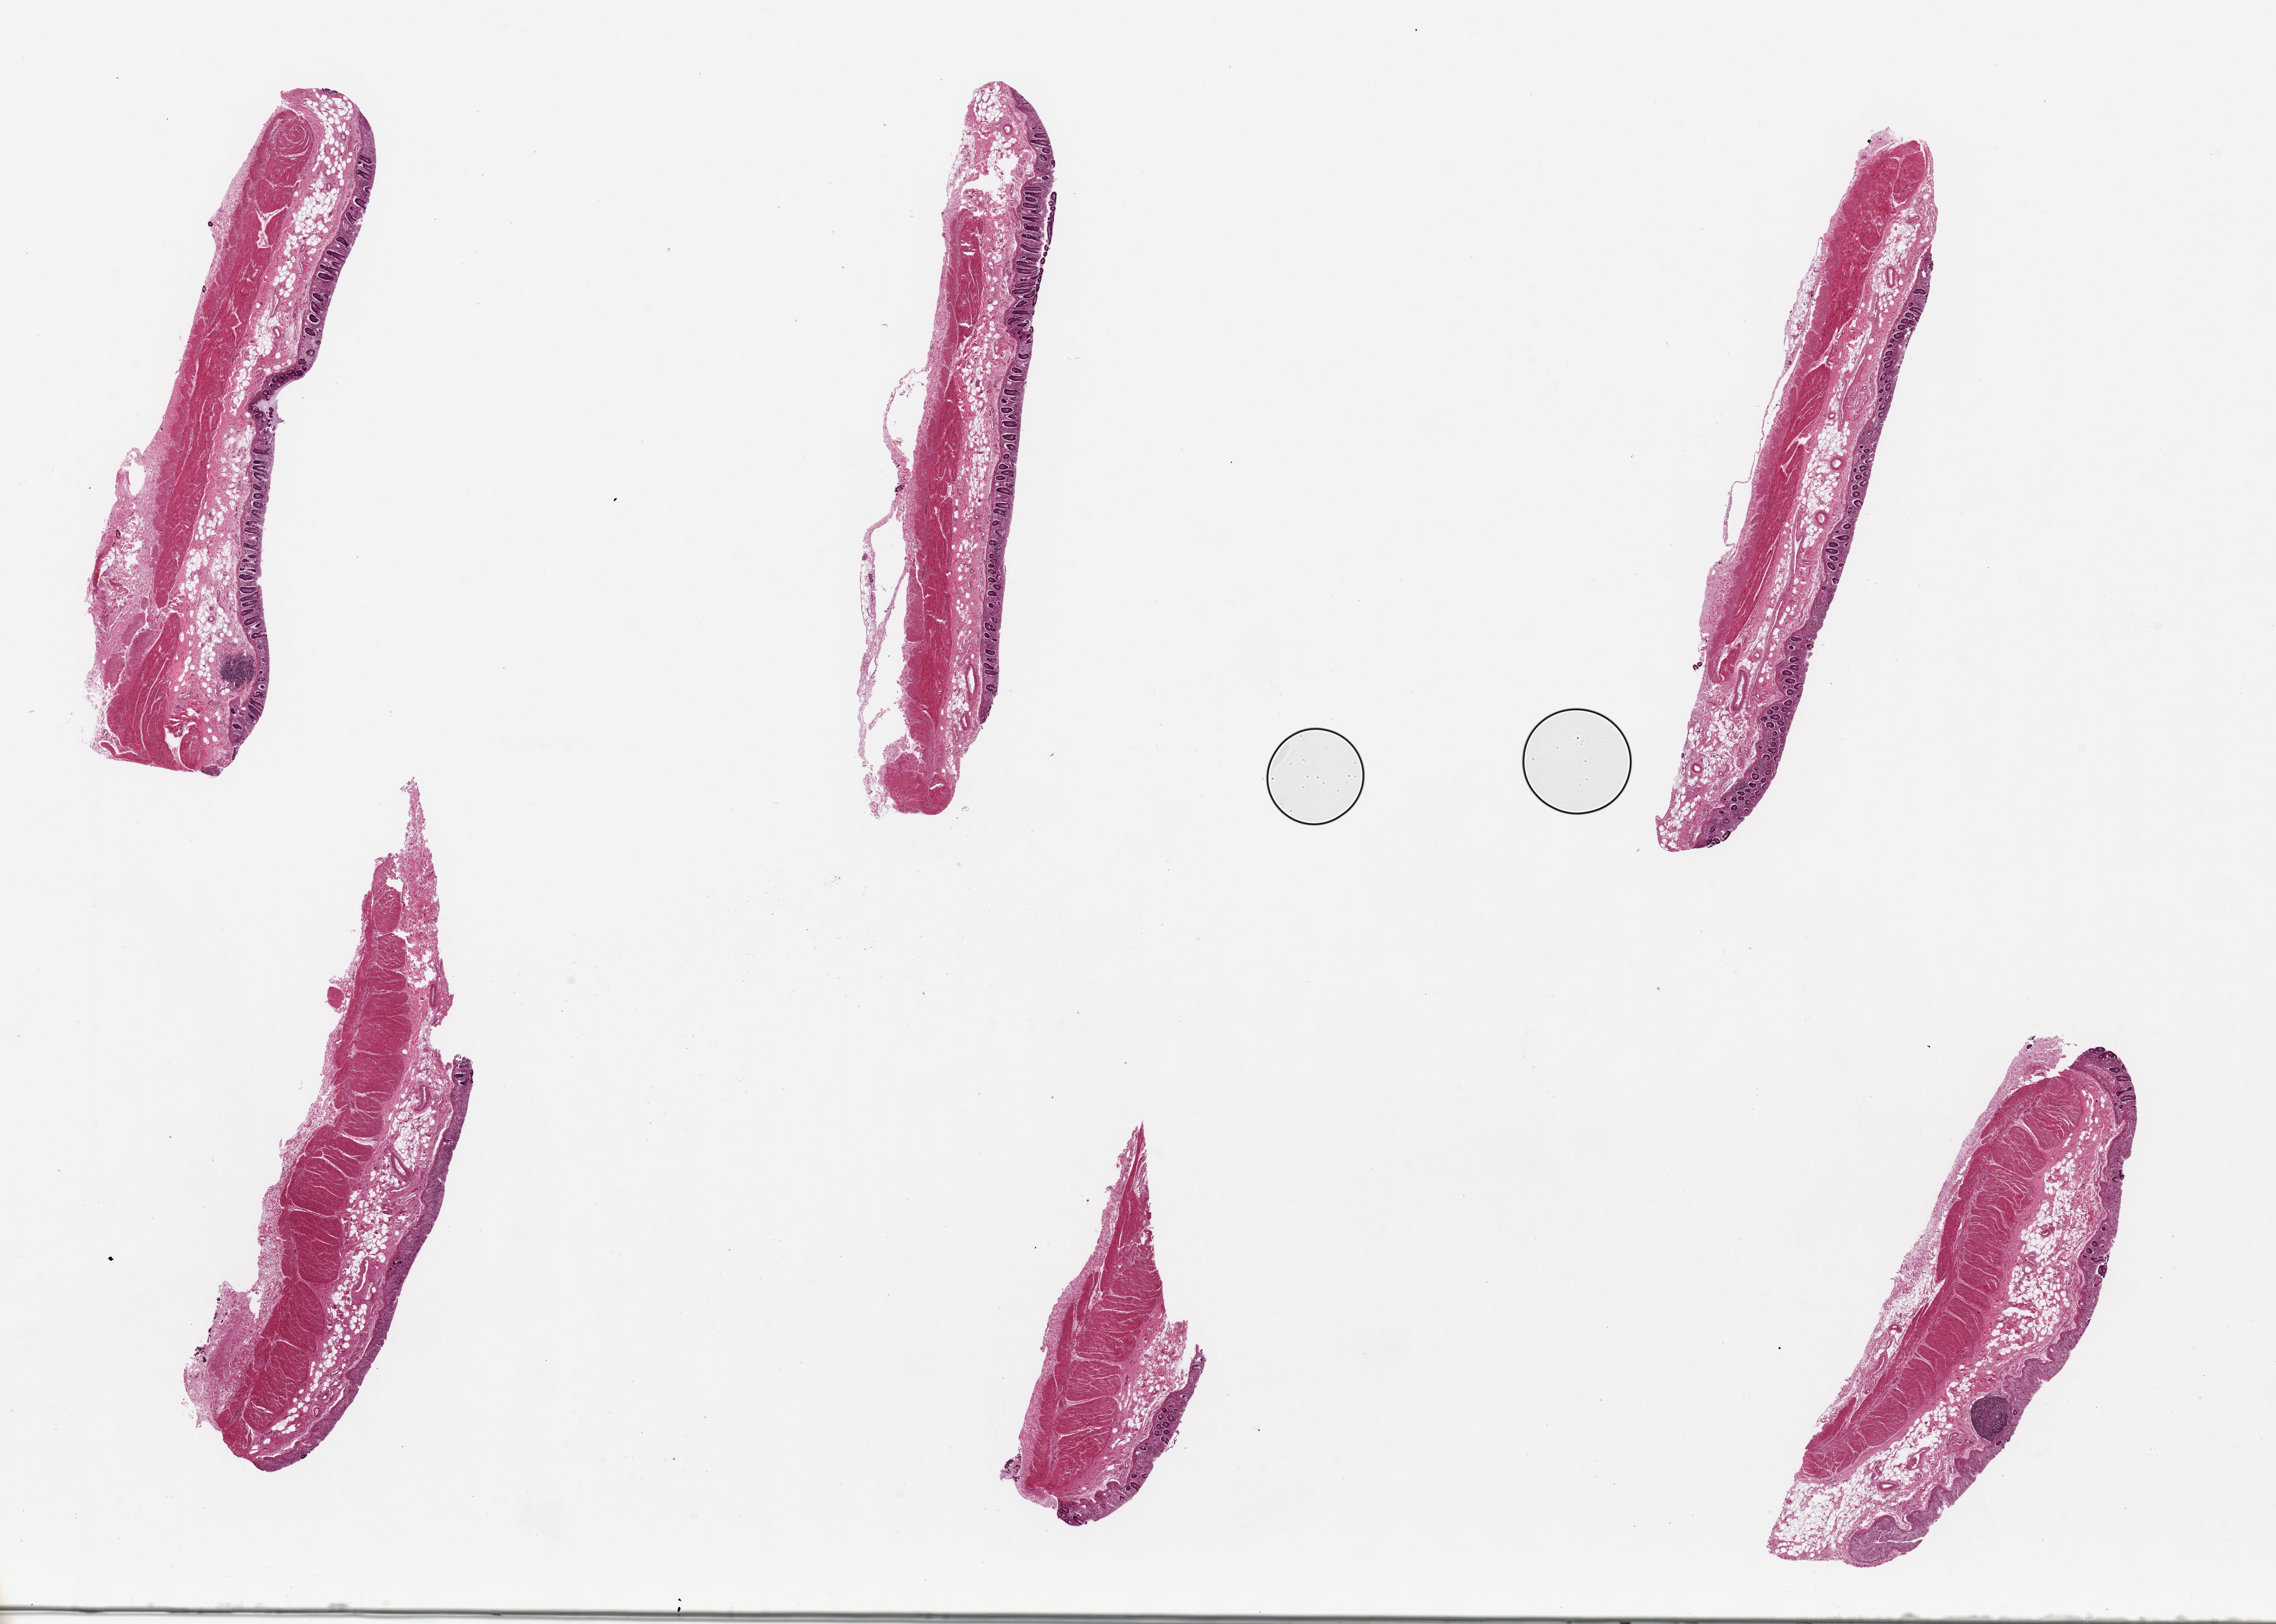
Whole-slide image, H&E stain, whole scanned area (about 29.5 x 21.1 mm, slide scanned at 20x) shown as a low-resolution overview. PAXgene-fixed, paraffin-embedded tissue. Target tissue: transverse colon. Tissue donor sample.
Pathologist's review note for this sample: 6 pieces, up to 10x2mm; poor preservation of mucosa; muscularis better preserved.